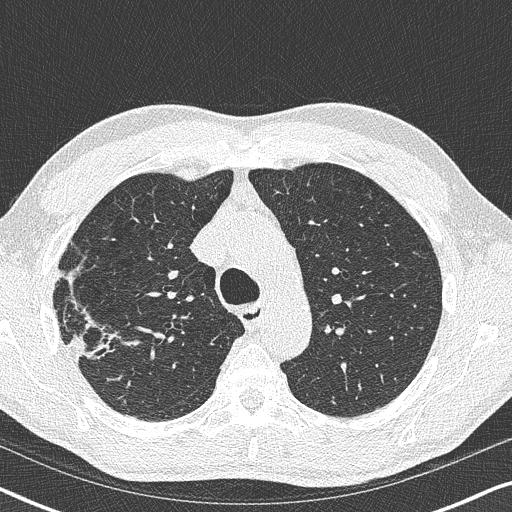
Low-dose screening chest CT, one axial slice. Slice 269 of 356 in the series (ordered by position). Lung window (W 1500 / L -600 HU). 1 mm slice thickness. 512 × 512 image matrix, field of view 330 × 330 mm.
Outlined on this slice (outlined manually by an expert reader):
- lesion 1 (tumor, upper lobe of right lung): bounding box <68,325,114,367> (left, top, right, bottom; pixels)